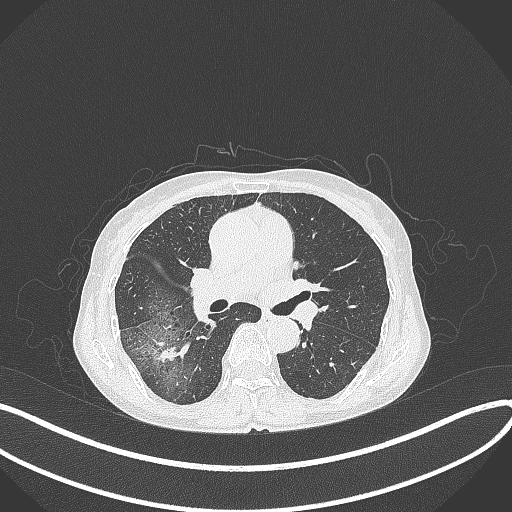
Chest CT, one axial slice. Slice 225 of 371 in the series (ordered by position). Reconstruction kernel B70f. Lung window (W 1500 / L -600 HU). 1 mm slice thickness. 512 × 512 image matrix. Patient: female, 69 years. From the clinical record (not read from this slice): clinical TNM (as recorded): T1b N0 M0; histopathological grade: G2-3.
Outlined on this slice (bounding box drawn by a radiologist):
- lung tumour (recorded histology: adenocarcinoma): bounding box <153,338,192,371> (left, top, right, bottom; pixels)